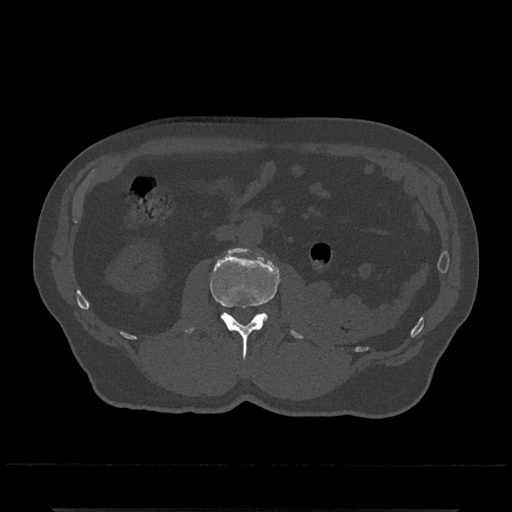
CT including the spine, one axial slice; position 284 of 797 along the scan axis; reconstruction kernel Br40s/3; bone window (W 1800 / L 400 HU); 512 × 512 image matrix, field of view 393 × 393 mm. Male patient, age 67 years. From the clinical record (not read from this slice): primary cancer: prostate.
Outlined on this slice (semi-automatically segmented with operator editing):
- L2 vertebra: bounding box [x1, y1, x2, y2] px = [185, 247, 304, 359]
- L3 vertebra: [260, 312, 265, 315]